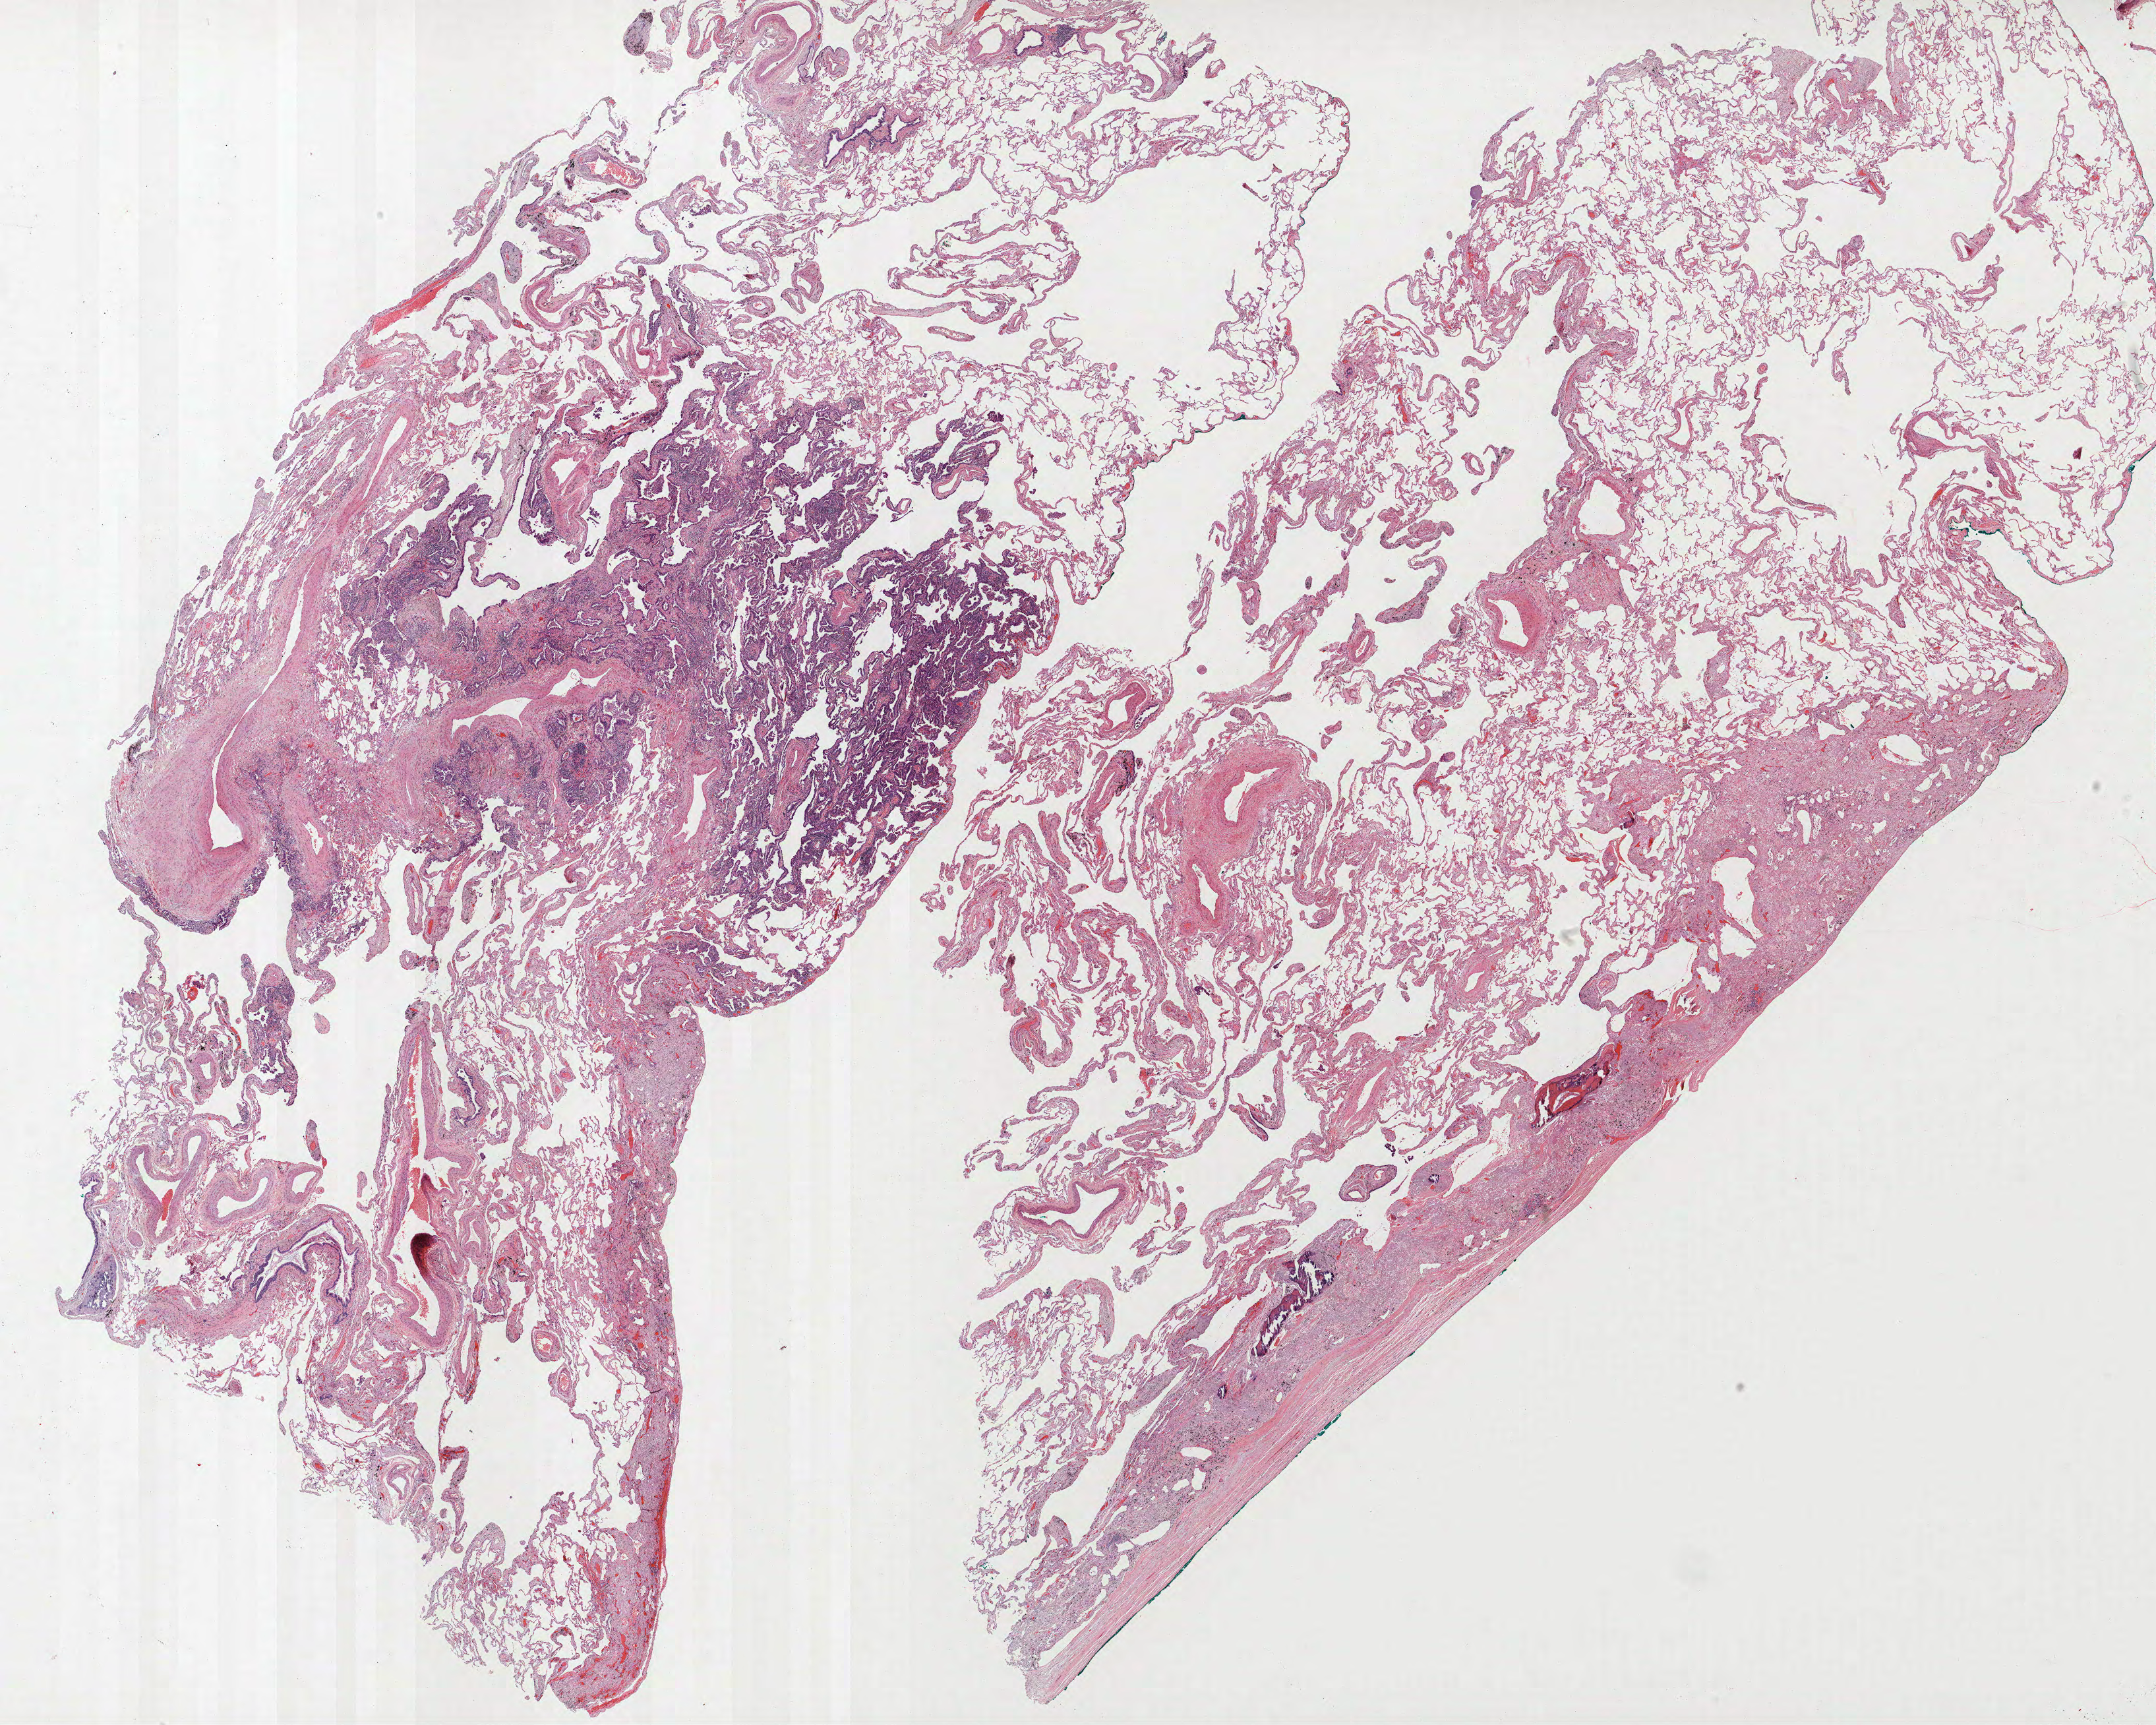
H&E-stained whole-slide image — shown as a low-resolution overview of the whole scanned area (about 26.2 x 20.9 mm). FFPE section. Lung tissue. Female patient, aged 73 at enrolment. Grade: moderately differentiated (G2).
- tumour size (pathology): 15 mm
- primary tumour location (clinical record): right upper lobe
- participant's lung-cancer diagnosis: Adenocarcinoma, NOS
- ICD-O-3 topography: upper lobe of lung (C34.1)
- stage (AJCC 6th edition): IB